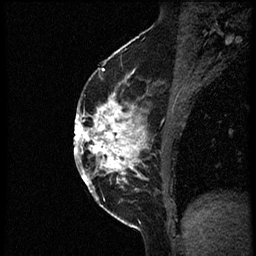
Breast MRI (dynamic contrast-enhanced), one sagittal slice. Slice 32 of 56 in the series (ordered by position). Dynamic contrast-enhanced study with each time point stored as its own series, time point 2 of 3 at this slice position (early post-contrast, ordered by acquisition time). 1.5 T. TE 4.2 ms, TR 21.3 ms. 2 mm slice thickness. 256 × 256 image matrix. Patient: female, 41 years. Case-level facts recorded for this patient, not image findings: setting: breast cancer imaged before/during neoadjuvant chemotherapy; receptor status: HER2-positive.
Annotated regions visible in this slice (semi-automatically segmented with operator editing):
- analysis volume of interest (the breast-tissue region the enhancement analysis was run in; not a lesion): bounding box <85,73,177,205> (left, top, right, bottom; pixels)
- tumour enhancement mask (voxels above the 100 % enhancement threshold inside the analysis volume of interest): <85,77,148,188>